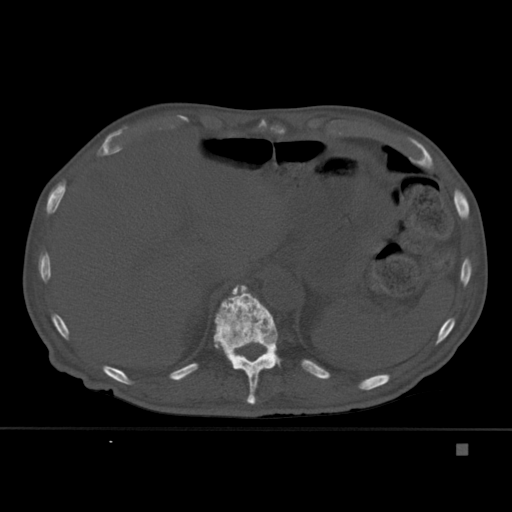
CT including the spine, one axial slice; bone window (W 1800 / L 400 HU); 1.5 mm slice thickness; 512 × 512 image matrix, field of view 378 × 378 mm. Patient: male, 75 years. Case-level facts recorded for this patient, not image findings: primary cancer: prostate.
Outlined on this slice (semi-automatically segmented with operator editing):
- T11 vertebra: box from (x=213, y=285) to (x=282, y=405) px
- T12 vertebra: (x=229, y=286)–(x=279, y=368)